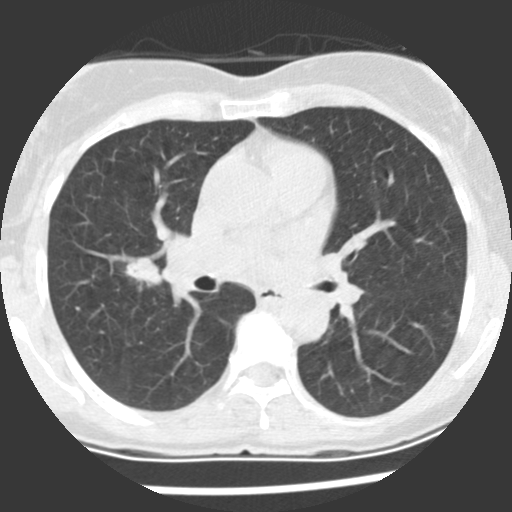
Chest CT (low-dose screening protocol), one axial image, first (baseline) screen, lung window (W 1500 / L -600 HU), 120 kVp, slice 104 of 225 in the series, 512 × 512 image matrix. Female, age 60 years at enrolment. Current smoker at enrolment.
- Lesion marked by an expert reader, bounding box (x1, y1, x2, y2) in pixels: (115, 253, 173, 299).
- The screening reader recorded 2 non-calcified nodules or masses ≥4 mm on this exam; which of them this box marks is not recorded.
- Lung cancer was diagnosed 10 days after this screen: adenocarcinoma, NOS, right upper lobe, stage IIIA (AJCC 6th edition), 20 mm at pathology.